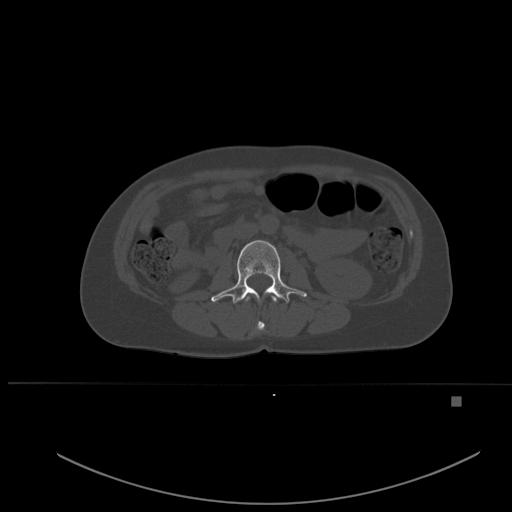
CT including the spine, one axial slice; slice 216 of 651 in the series (ordered by position); bone window (W 1800 / L 400 HU); 512 × 512 image matrix, field of view 443 × 443 mm. Female patient, age 49 years. From the clinical record (not read from this slice): primary cancer: breast.
Structures marked on this image (semi-automatic segmentation, software-assisted and operator-edited):
- L1 vertebra: bounding box [x1, y1, x2, y2] px = [246, 295, 277, 330]
- L2 vertebra: [211, 240, 307, 304]